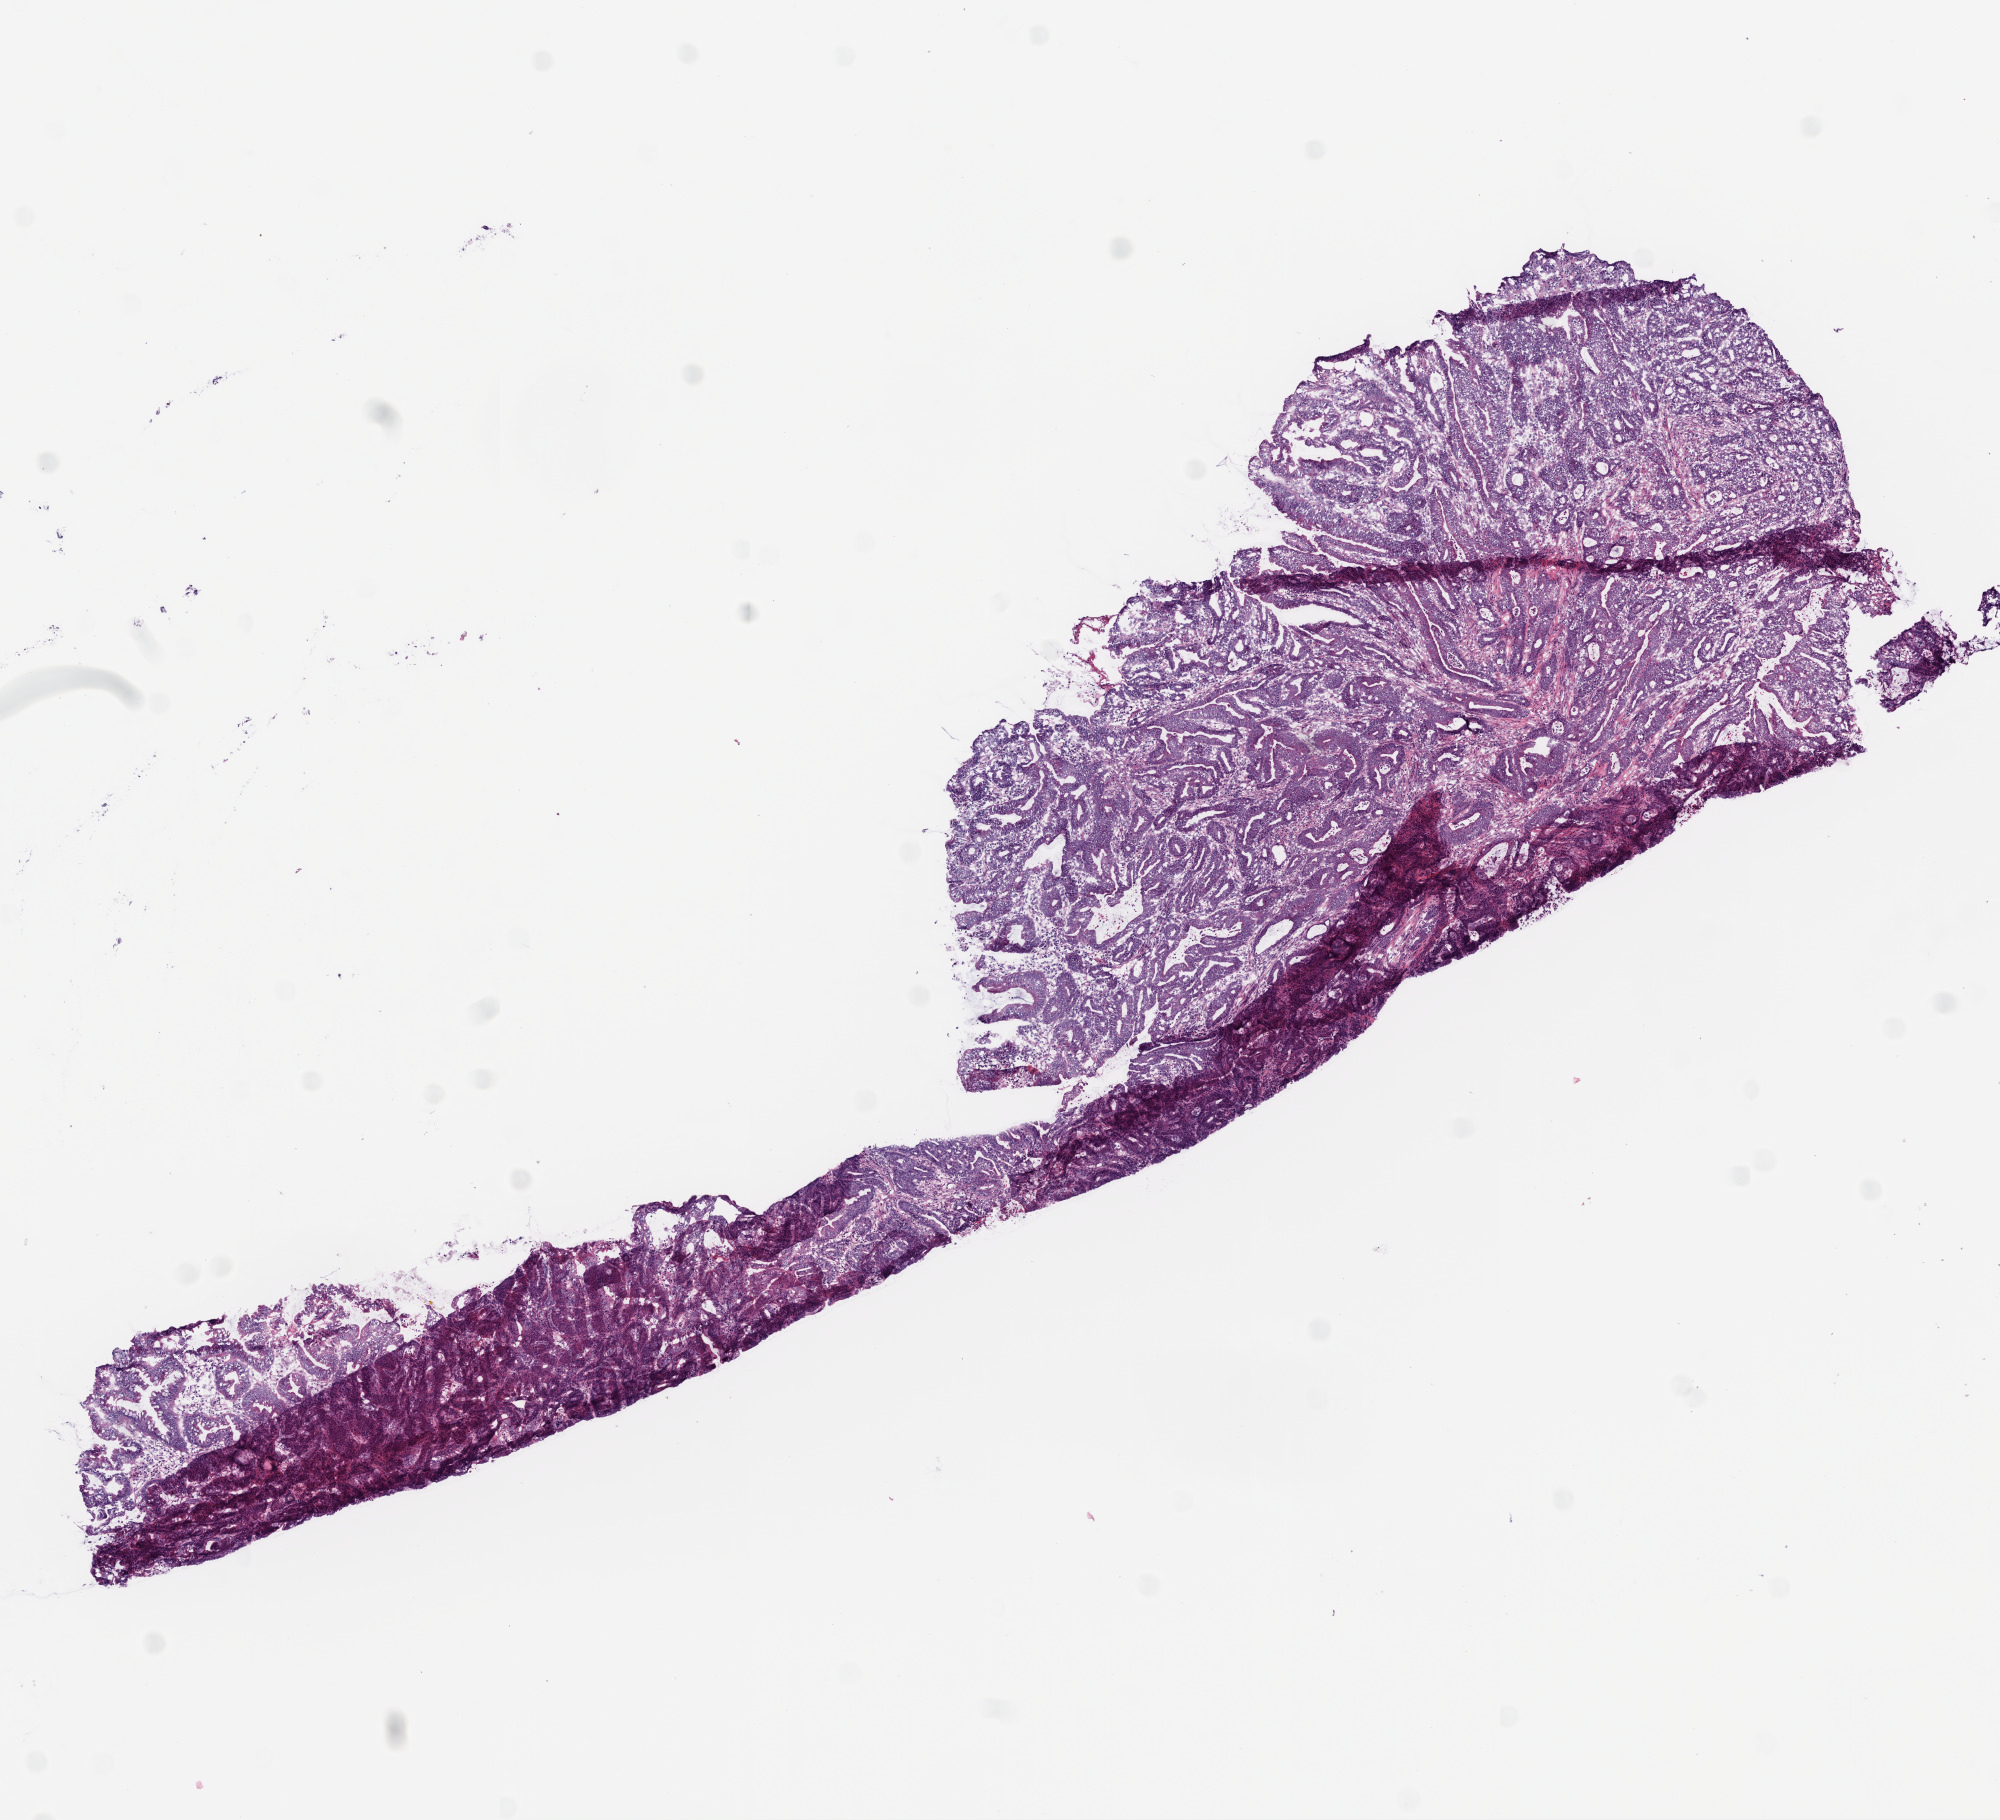
H&E-stained whole-slide image, a low-resolution overview of the entire scanned area, about 8.0 x 7.3 mm (acquisition: 20x scan), frozen section from the bottom of the tissue portion, colon, primary tumour sample. Male, age 84 years at initial diagnosis. Pathologist review of this section (percent, as recorded): tumour cells 60%, tumour nuclei 70%, normal cells 0%, stromal cells 38%, necrosis 2%.
• TNM: T2 N0 M0
• AJCC pathologic stage: I (6th edition)
• pathologic diagnosis: Mucinous adenocarcinoma (ascending colon)